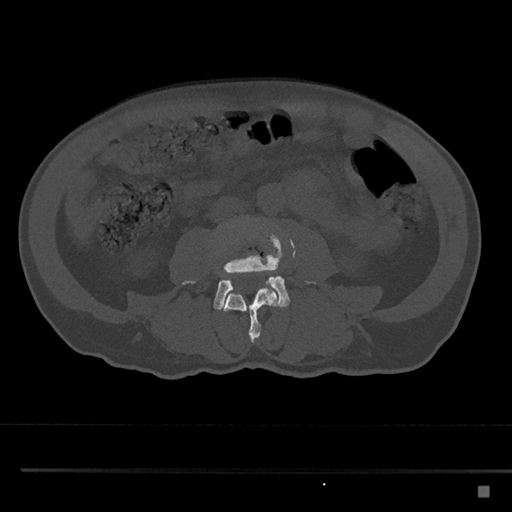
CT including the spine, one axial slice. Position 665 of 797 along the scan axis. Reconstruction kernel Br40s/3. 120 kVp. Bone window (W 1800 / L 400 HU). 0.5 mm slice thickness. 512 × 512 image matrix, field of view 391 × 391 mm. Male patient, age 59 years. Case-level facts recorded for this patient, not image findings: primary cancer: prostate.
Outlined on this slice (semi-automatically segmented with operator editing):
- L3 vertebra: bounding box <221,284,280,342> (left, top, right, bottom; pixels)
- L4 vertebra: <182,226,317,310>